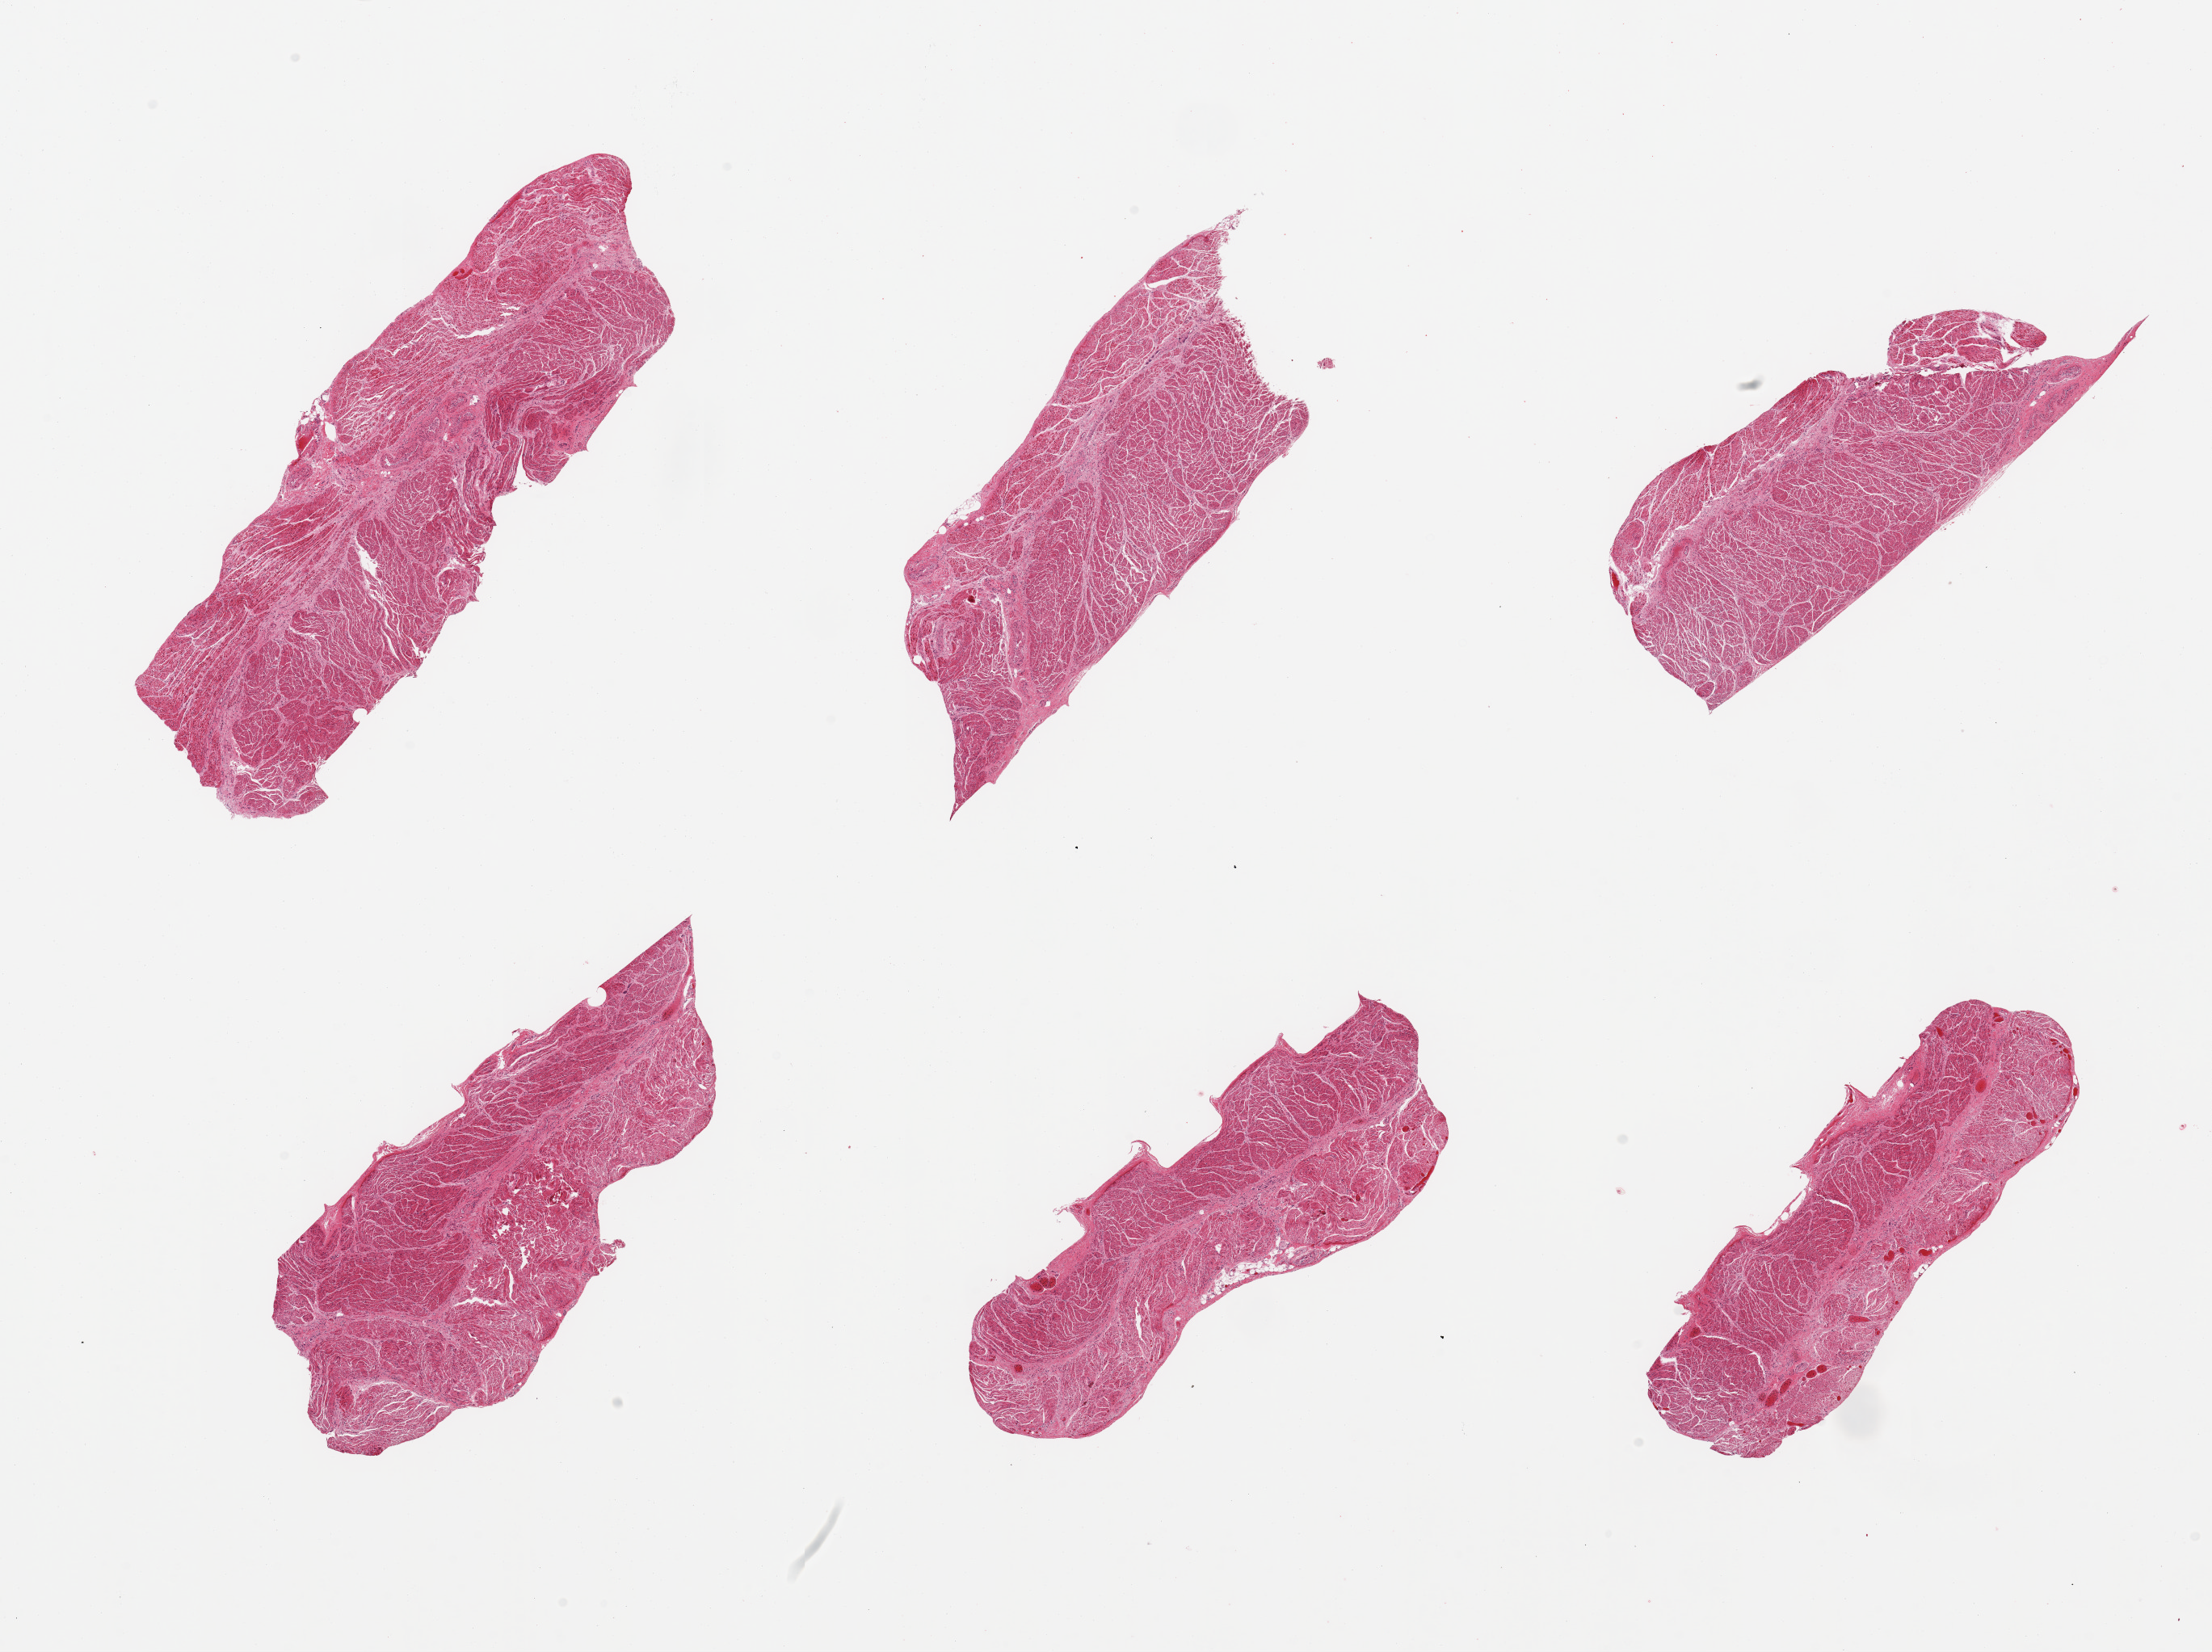
Digitized H&E-stained section, brightfield — a low-resolution overview of the entire scanned area, about 21.7 x 16.2 mm, PAXgene-fixed, paraffin-embedded tissue, target tissue: gastroesophageal junction, tissue donor sample. Female donor.
Review note (as recorded): 6 pieces; well dissected.